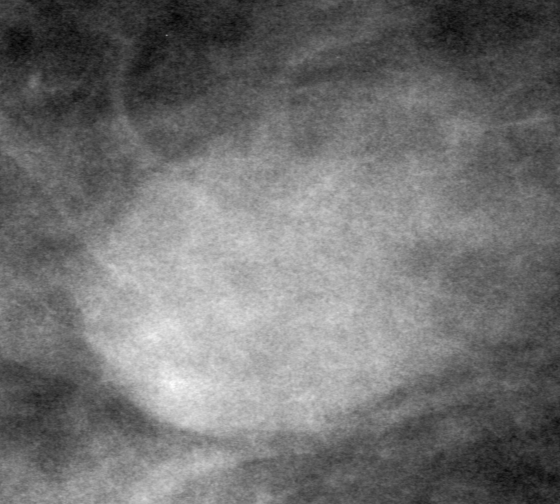
Crop from a digitized film mammogram around one marked abnormality, right breast, MLO view, BI-RADS breast density category 3 (scale 1–4).
Marked abnormality: mass, shape oval, margins obscured; BI-RADS assessment category 0 (incomplete: needs additional imaging); subtlety rating 4 on a 1 (subtle) to 5 (obvious) scale; pathology (as recorded): benign.